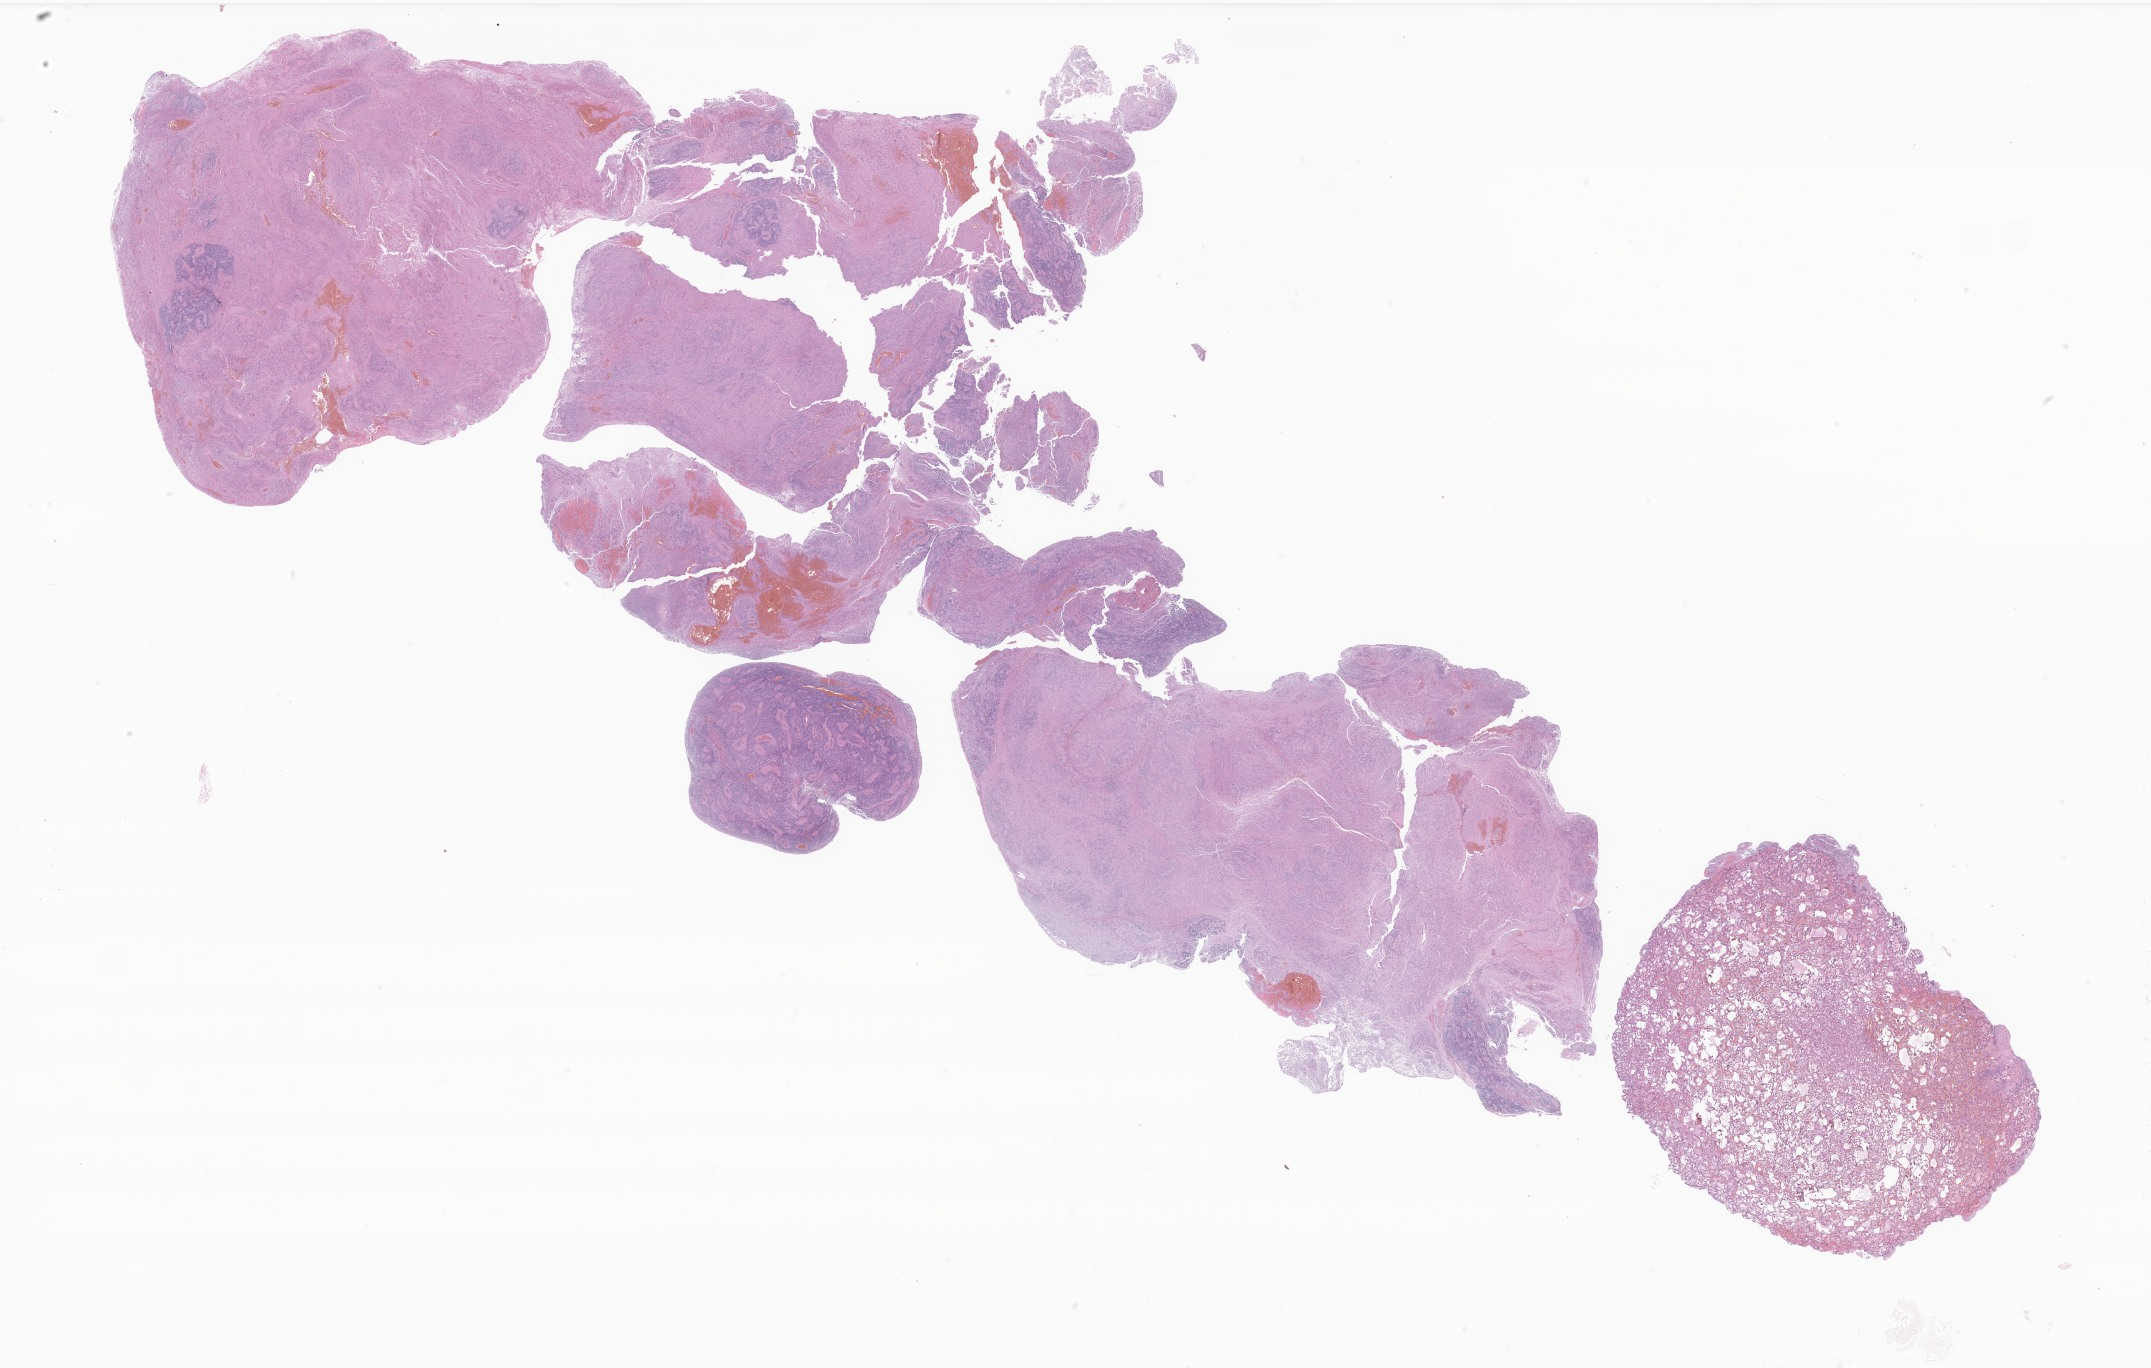
Digitized haematoxylin and eosin-stained section of tumor tissue from the brain — whole scanned area (about 36.3 x 23.1 mm) shown as a low-resolution overview. Formalin-fixed, paraffin-embedded (FFPE) tissue. Male patient, age 51 months (4 years 3 months).
Diagnosis (ICD-O-3 morphology term): Ependymoma, anaplastic.